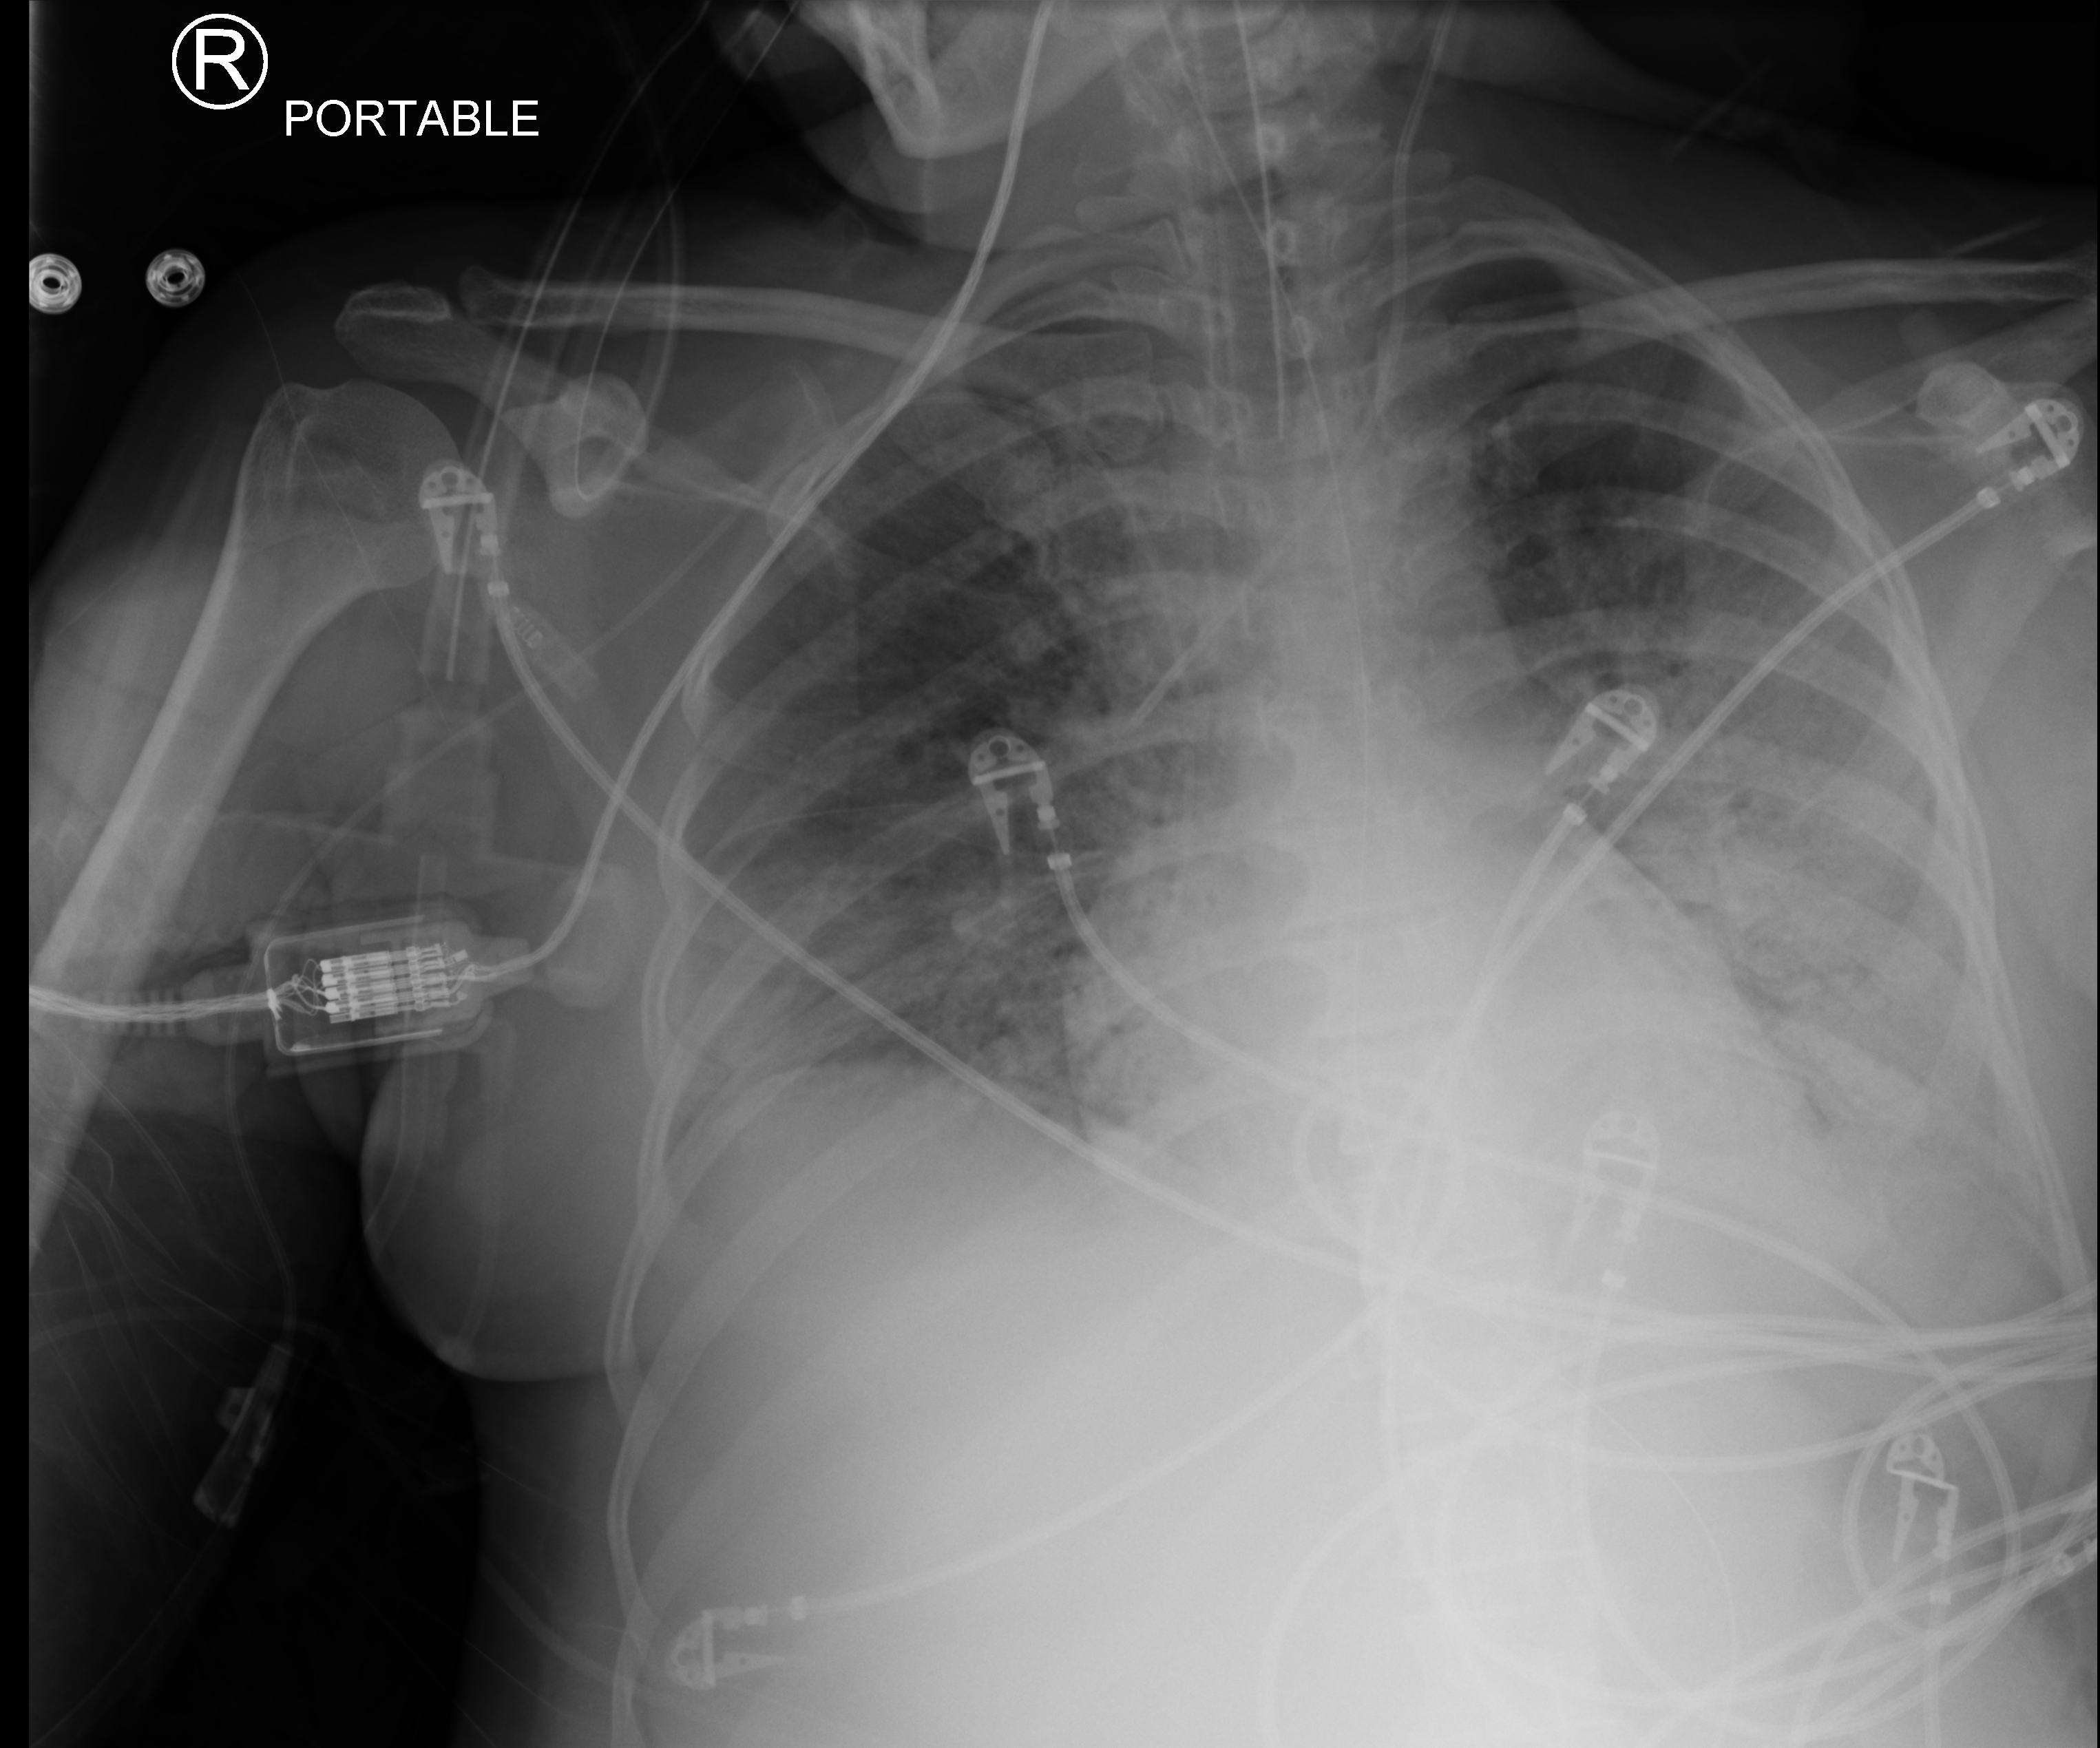
Bedside chest radiograph (computed radiography), anteroposterior (AP) projection. Female patient hospitalised with COVID-19, age 18–59 years.
Hospital-stay facts (about this admission, not read from this image; timing relative to this image not recorded):
- COPD (admission record): no